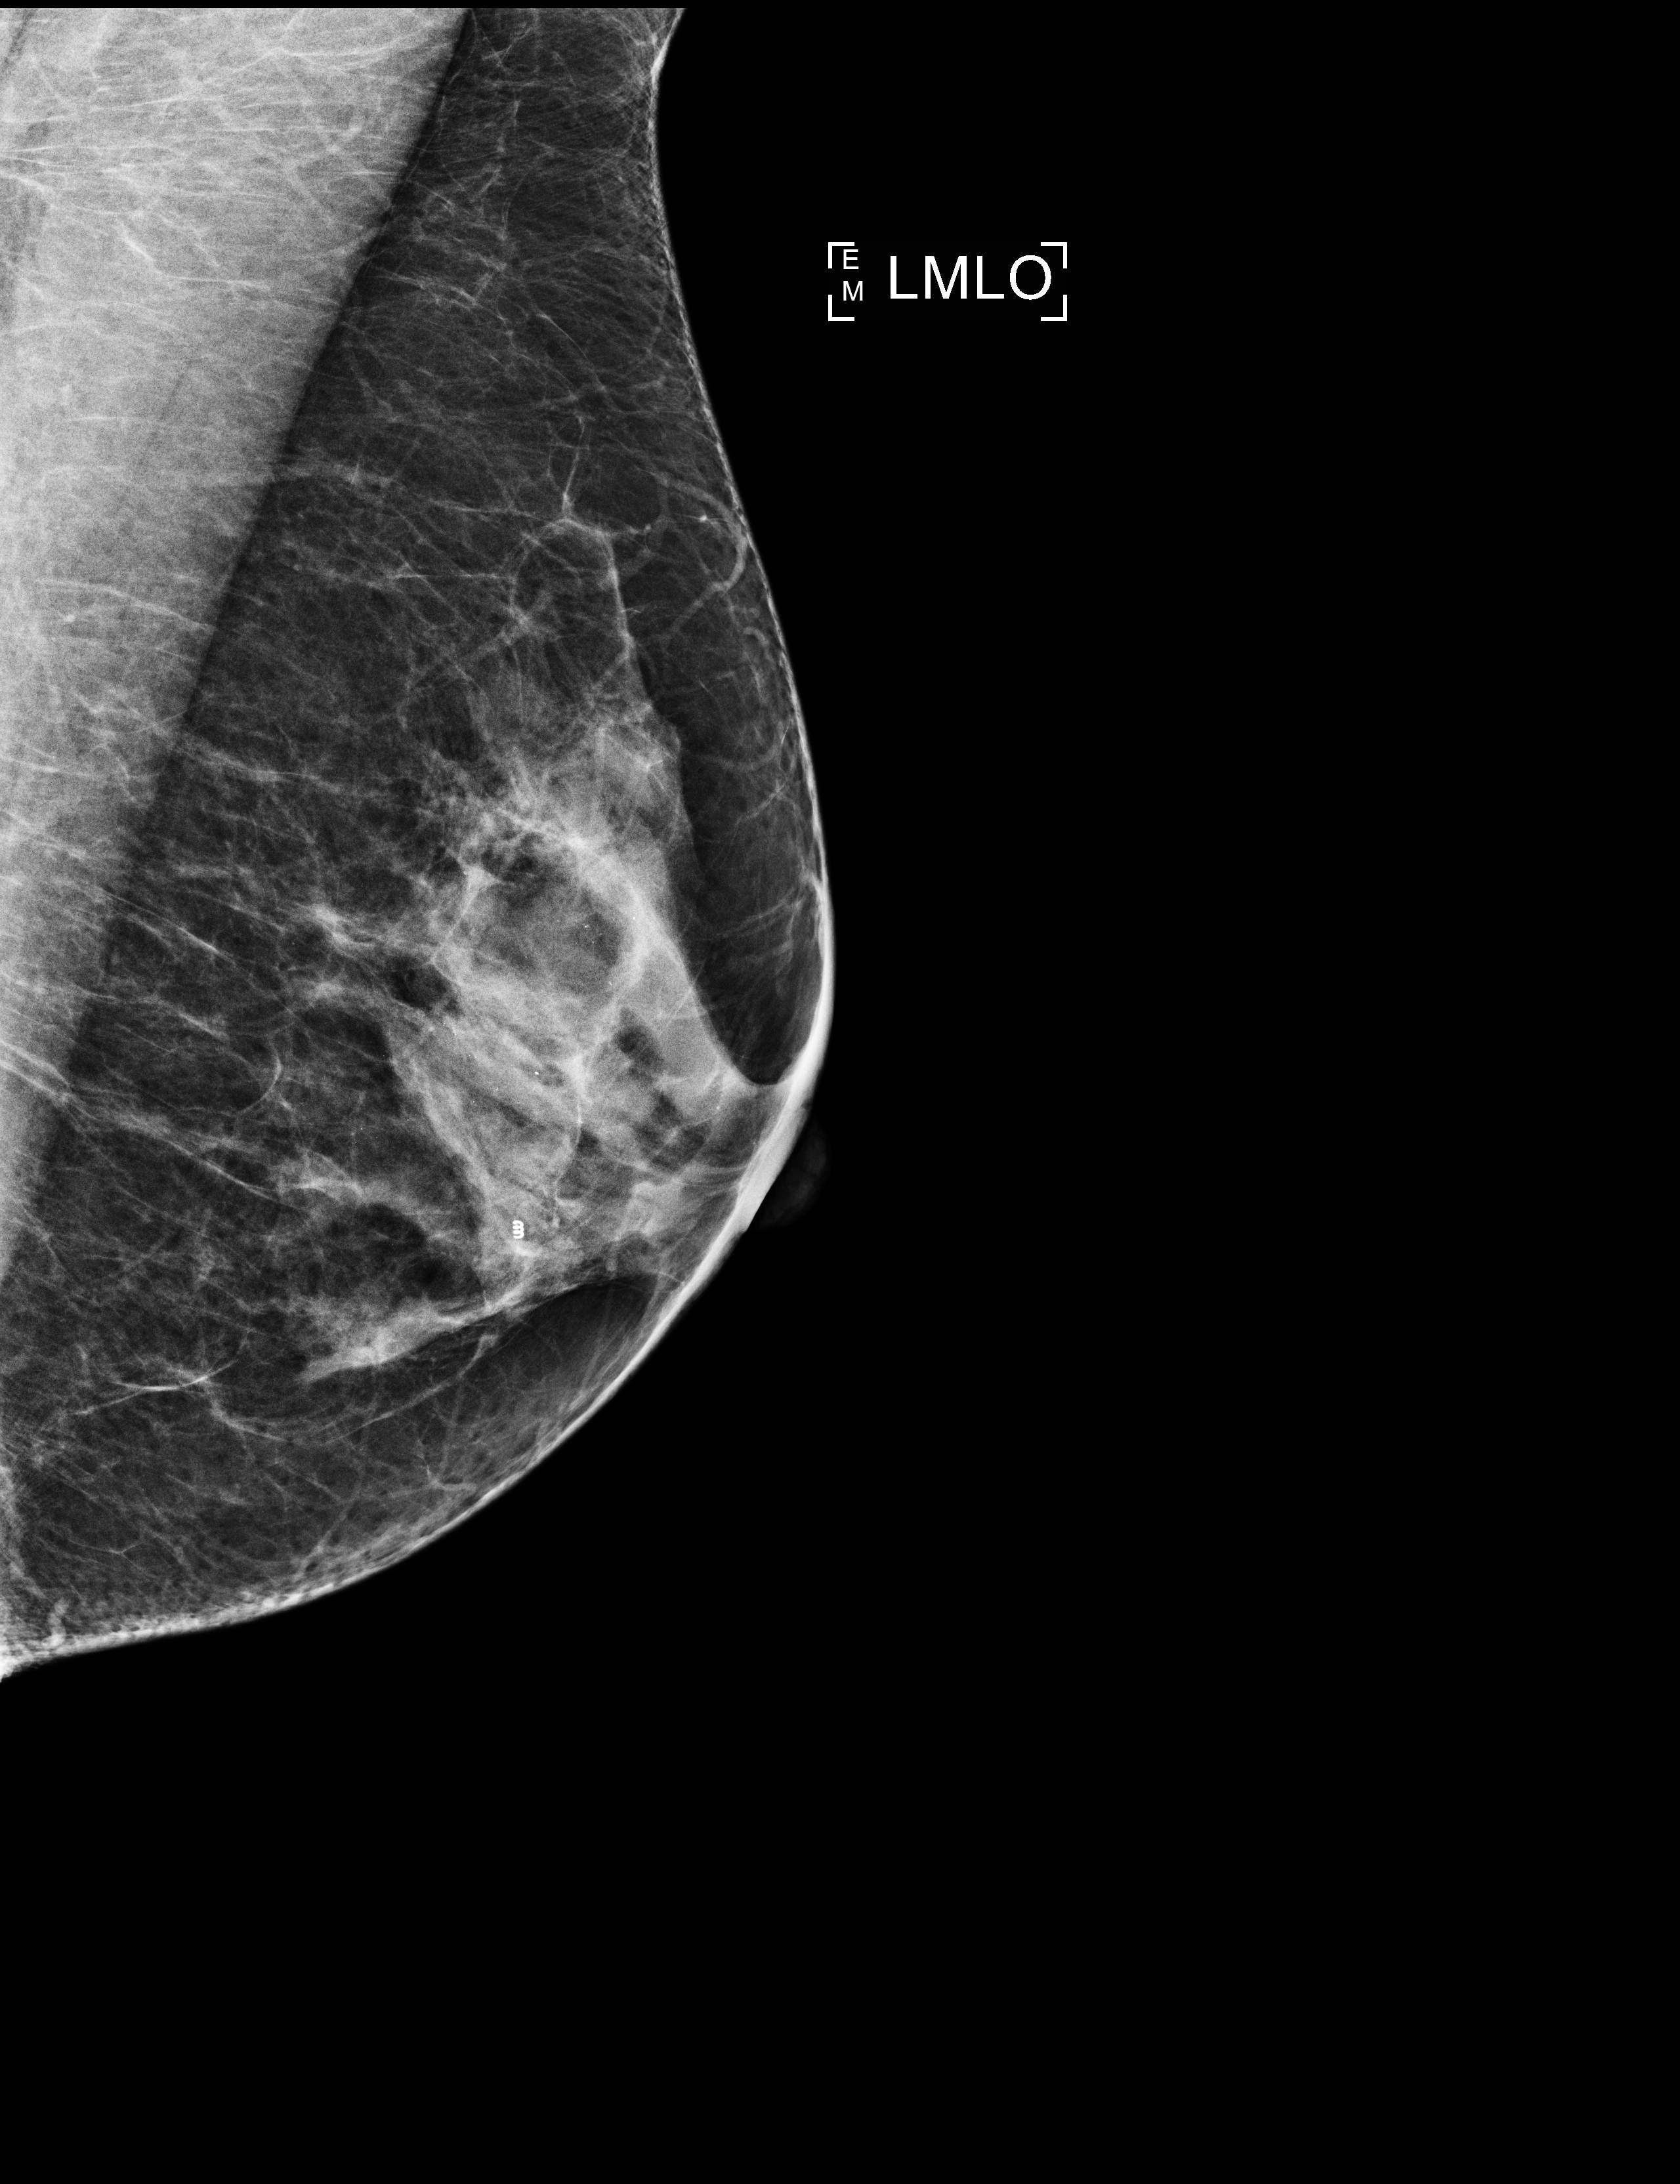
Digital mammogram (FFDM); left breast; MLO view; screening examination; compressed breast thickness 56 mm. Patient aged 56 years (female).
Final BI-RADS assessment for this screening round (tomosynthesis exam, both breasts): category 2.